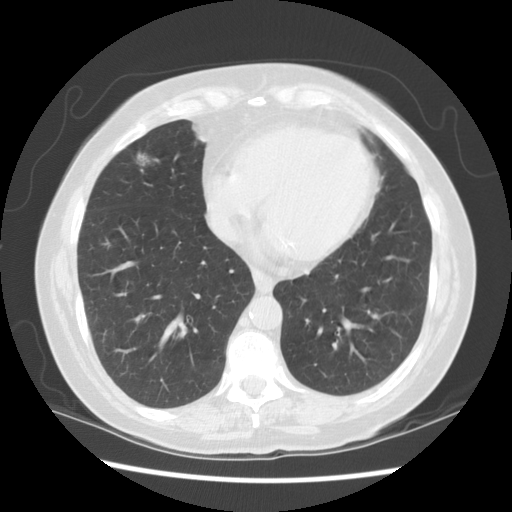
Low-dose screening chest CT, one axial slice; slice 43 of 115 in the series (ordered by position); reconstruction kernel STANDARD; 140 kVp; lung window (W 1500 / L -600 HU); 2.5 mm slice thickness; 512 × 512 image matrix, field of view 340 × 340 mm.
Annotated regions visible in this slice (manually delineated by an expert):
- lesion 1 (tumor, middle lobe of right lung): bounding box <137,153,149,166> (left, top, right, bottom; pixels)